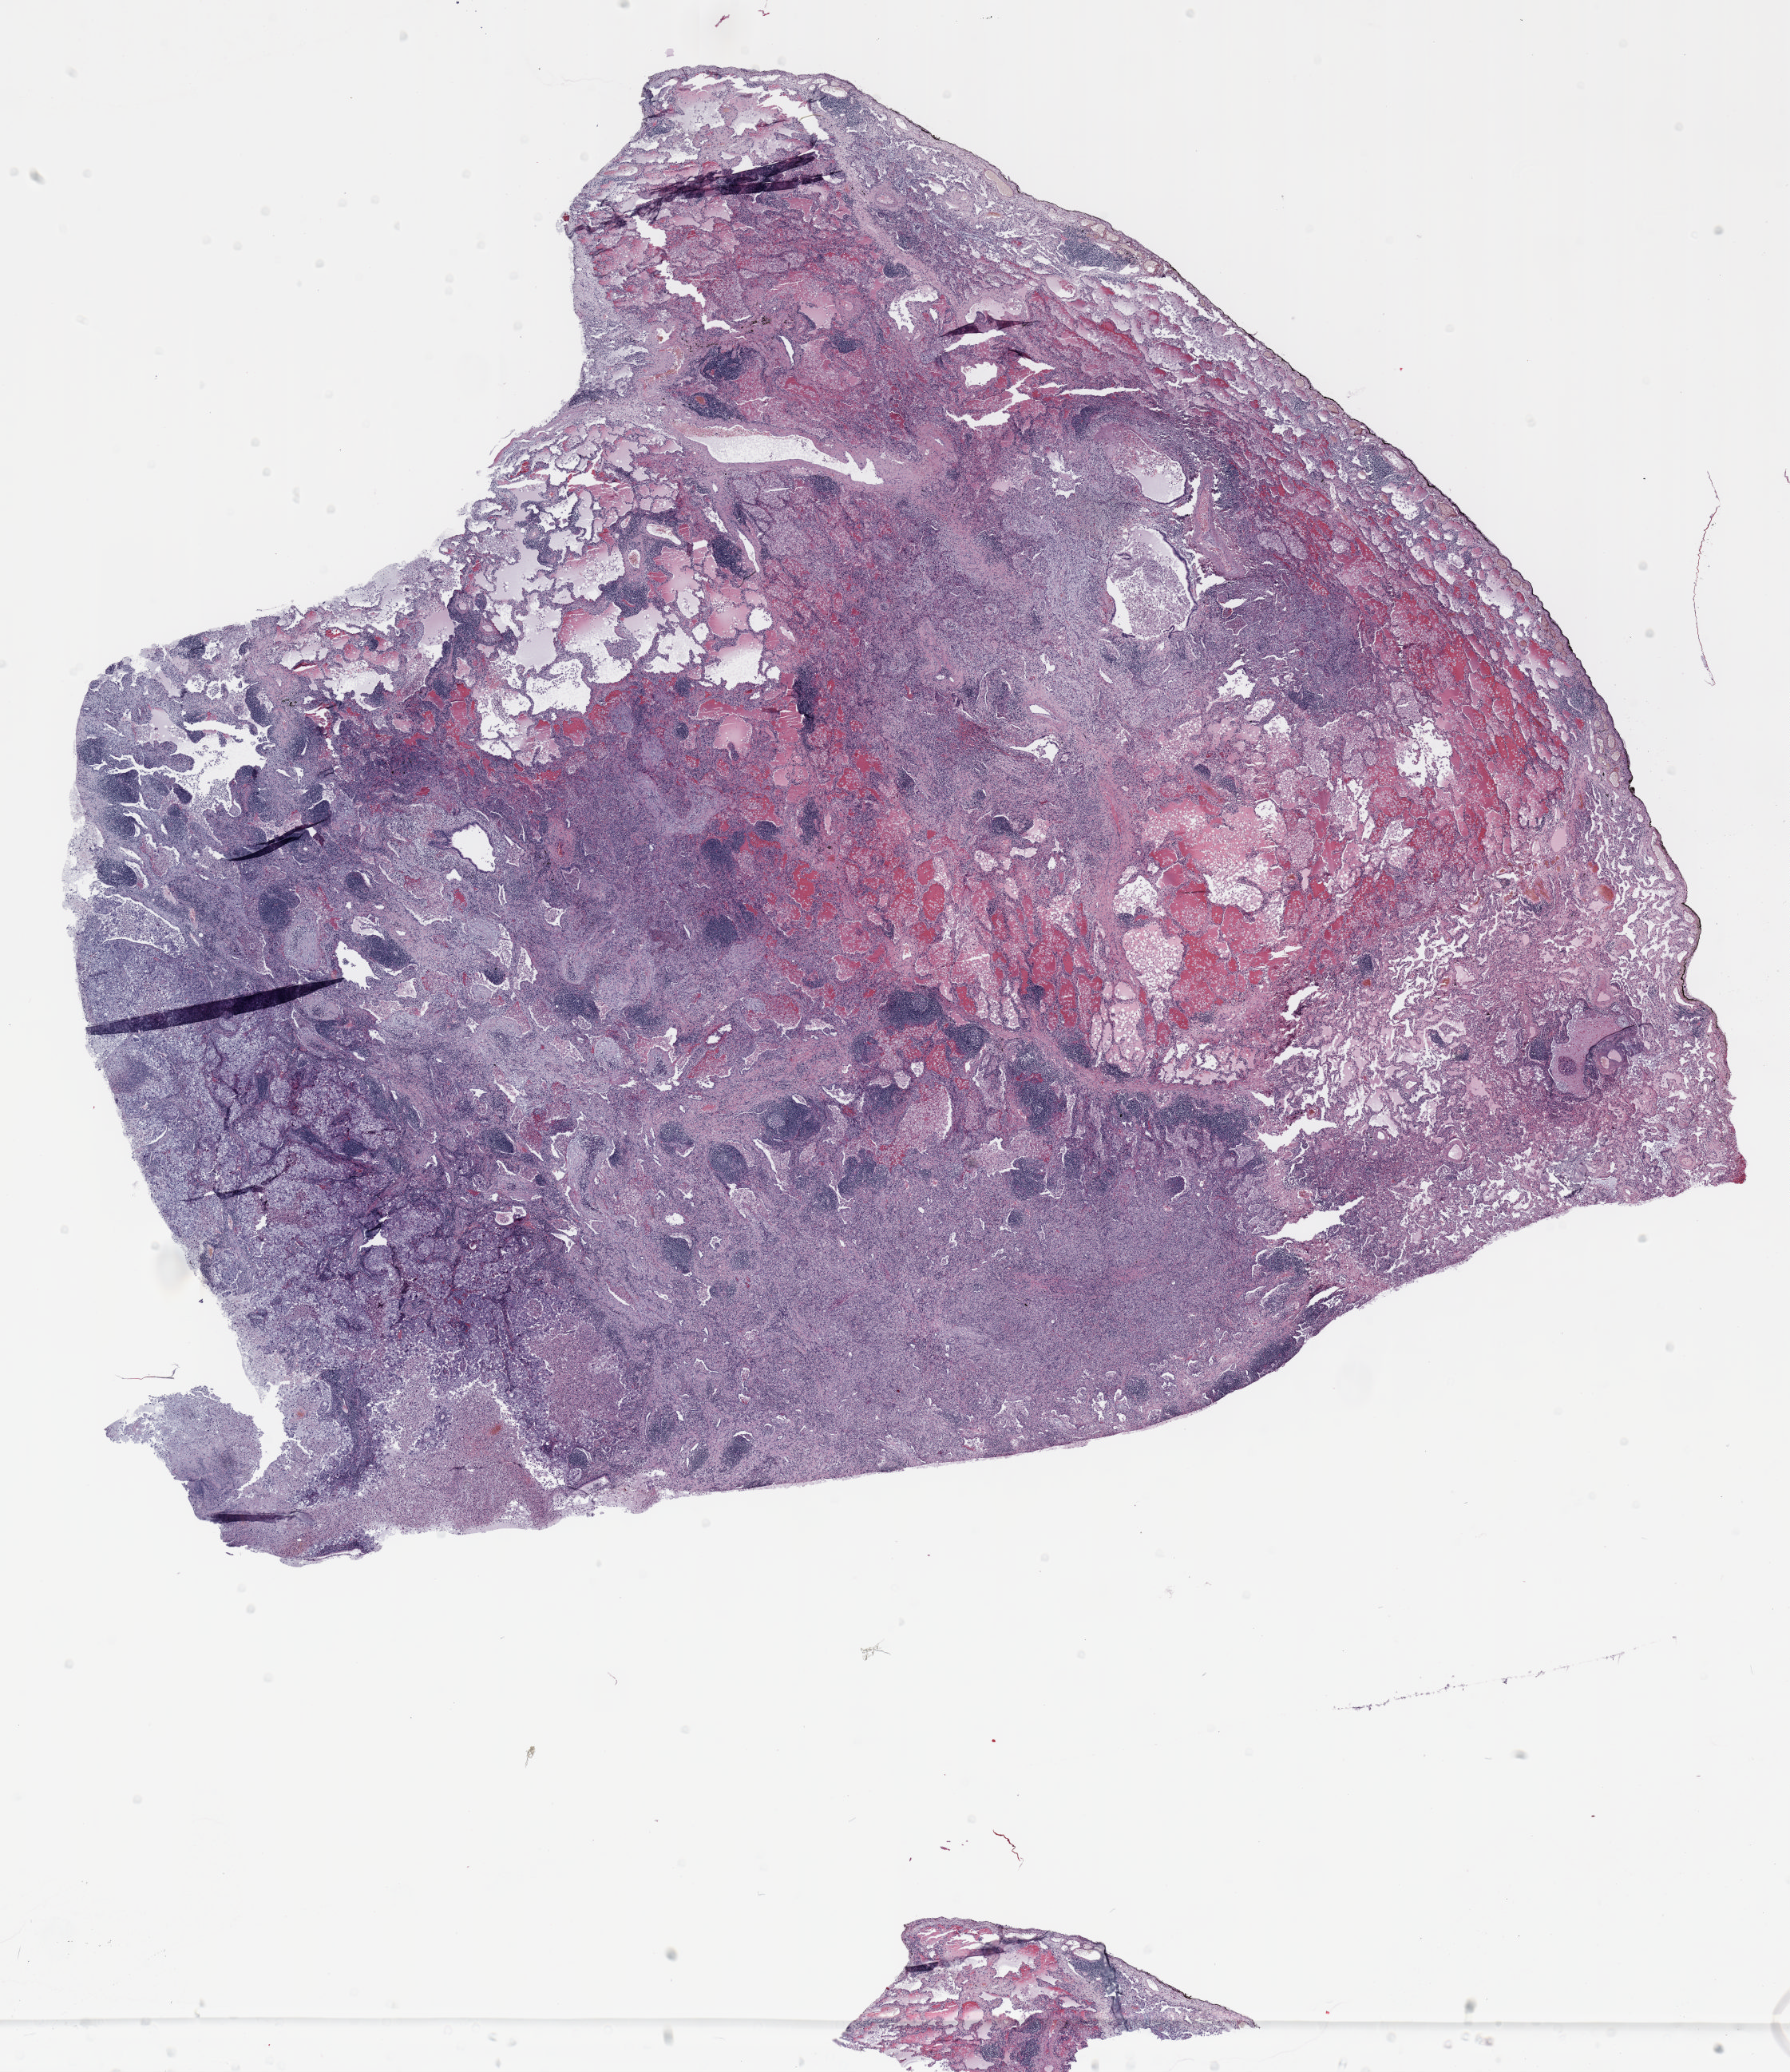
Whole-slide histology image, H&E-stained, low-resolution overview of the scanned area, about 18.0 x 20.9 mm. Formalin-fixed paraffin-embedded (FFPE) section. Lung. Female patient, aged 58 at enrolment. Former smoker at enrolment.
Participant's lung-cancer diagnosis: Large cell carcinoma, NOS (ICD-O-3 8012/3).